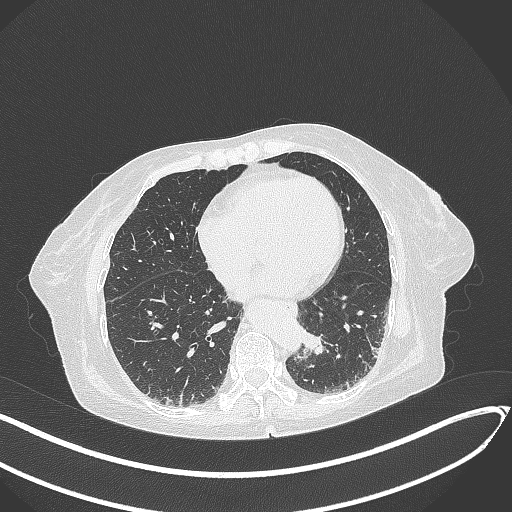
Chest CT, one axial slice; reconstruction kernel B70f; 120 kVp; lung window (W 1500 / L -600 HU); 512 × 512 image matrix. Patient: female, 82 years. Case-level facts recorded for this patient, not image findings: clinical TNM (as recorded): T1b N0 M1.
Outlined on this slice (bounding box drawn by a radiologist):
- lung tumour (recorded histology: adenocarcinoma): bounding box [x1, y1, x2, y2] px = [300, 325, 330, 361]